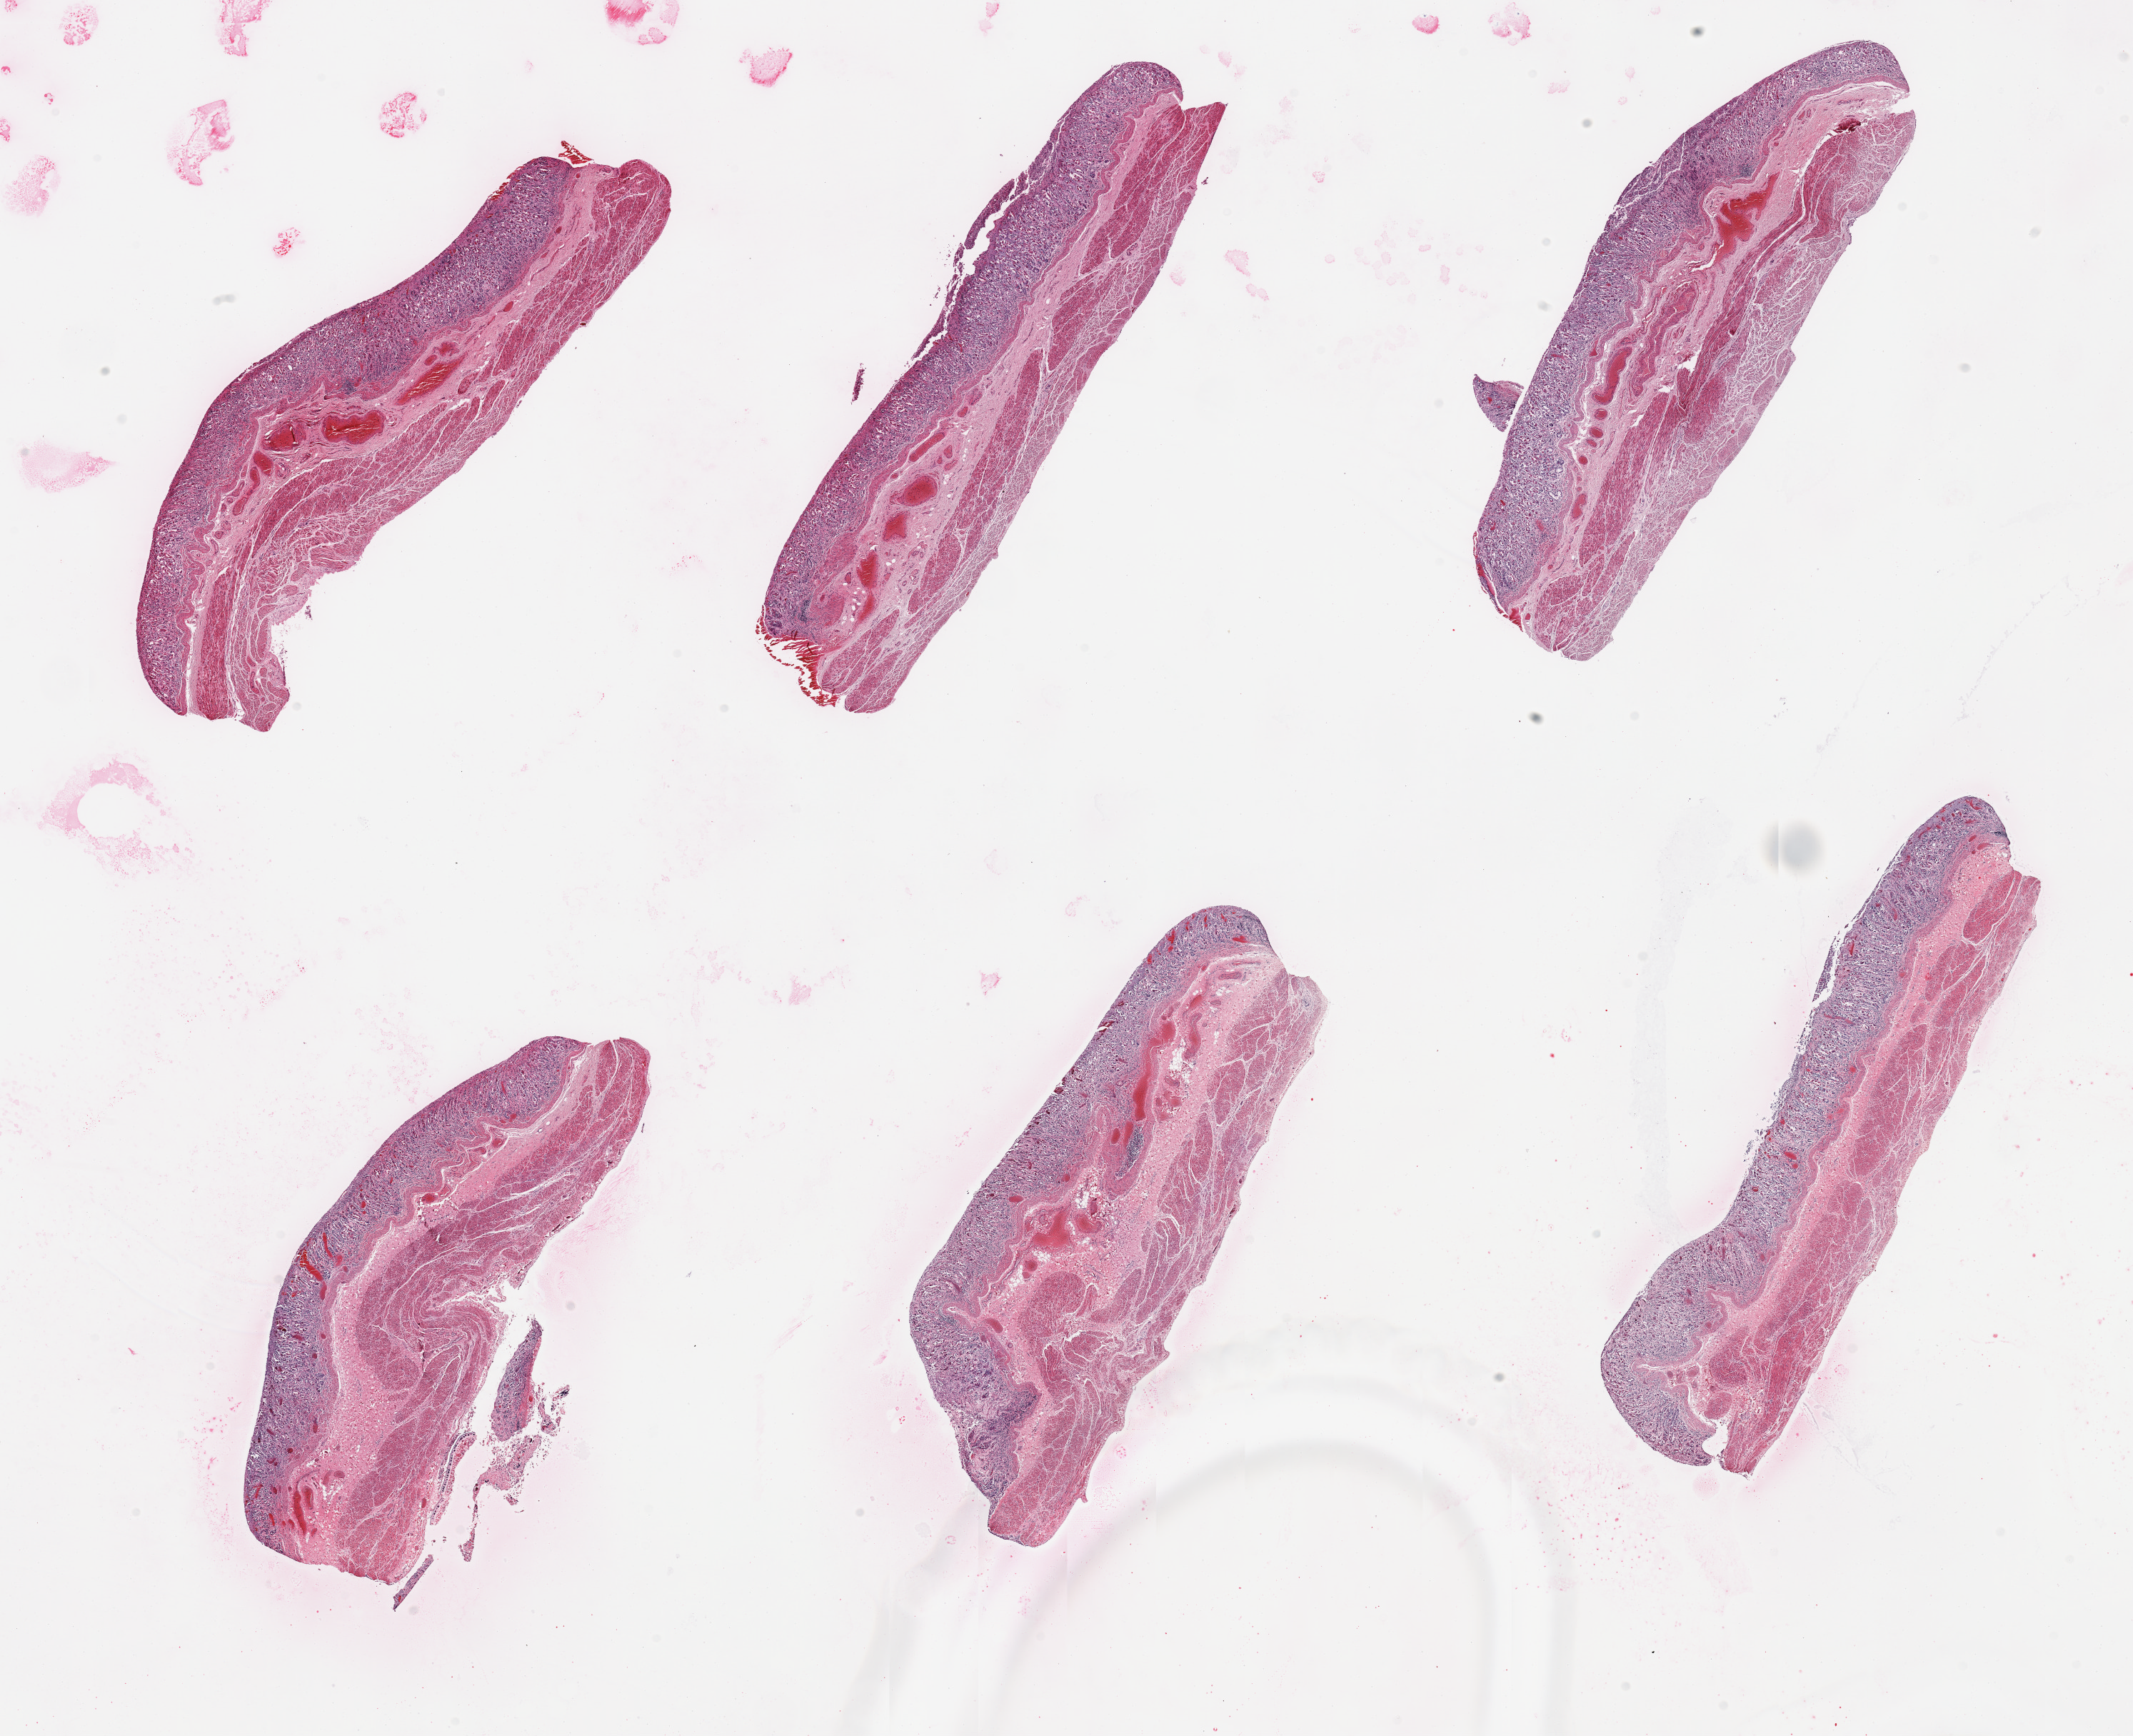
Whole-slide image, hematoxylin and eosin (H&E) stain — shown as a low-resolution overview of the whole scanned area (about 23.6 x 19.2 mm, slide scanned at 20x). PAXgene-fixed paraffin-embedded (PFPE) section. Target tissue: stomach. Donor tissue sample.
Pathologist's review note for this sample: 6 pieces; mucosa autolyzed, muscle intact.